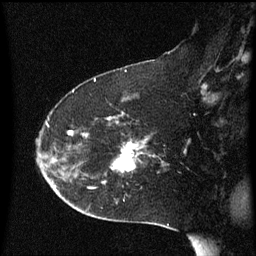
Breast MRI (dynamic contrast-enhanced), one sagittal slice; position 38 of 60 along the scan axis; dynamic contrast-enhanced series, image 2 of 3 at this slice position (ordered by acquisition); 1.5 T; TE 4.2 ms, TR 8.4 ms; 2 mm slice thickness; 256 × 256 image matrix. Patient: female, 54 years. From the clinical record (not read from this slice): setting: breast cancer imaged before/during neoadjuvant chemotherapy; receptor status: HR-positive, HER2-negative.
Structures marked on this image (semi-automatically segmented with operator editing):
- analysis volume of interest (the breast-tissue region the enhancement analysis was run in; not a lesion): bounding box (x1, y1, x2, y2) in pixels: (103, 120, 170, 183)
- tumour enhancement mask (voxels above the 70 % enhancement threshold inside the analysis volume of interest): (104, 144, 136, 183)